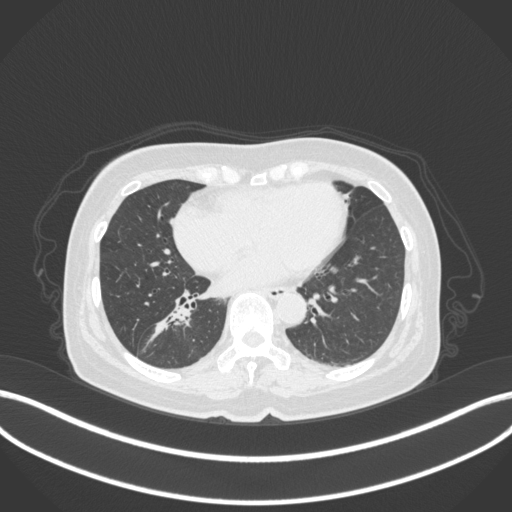
Chest CT, one axial slice. Position 156 of 429 along the scan axis. 120 kVp. Lung window (W 1500 / L -600 HU). 1 mm slice thickness. 512 × 512 image matrix. Patient: female, 67 years. Case-level facts recorded for this patient, not image findings: clinical TNM (as recorded): T1c N1 M0; histopathological grade: G2-3.
Structures marked on this image (rectangle marked by the reading radiologist):
- lung tumour (recorded histology: adenocarcinoma): box from (x=147, y=300) to (x=194, y=337) px